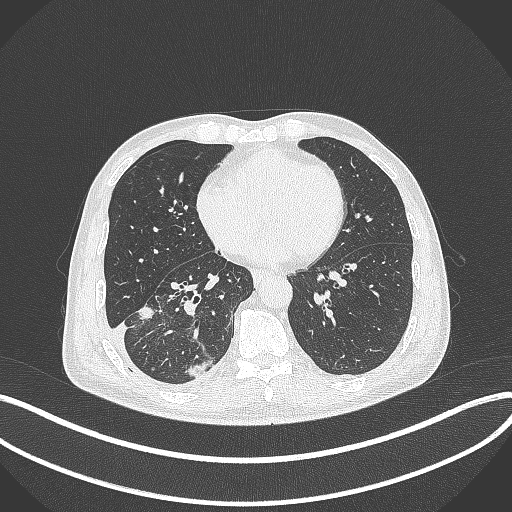
Chest CT, one axial slice. Position 148 of 388 along the scan axis. 120 kVp. Lung window (W 1500 / L -600 HU). 512 × 512 image matrix. Male patient, age 64 years. Case-level facts recorded for this patient, not image findings: clinical TNM (as recorded): T3 N0 M0.
Outlined on this slice (bounding box drawn by a radiologist):
- lung tumour (recorded histology: adenocarcinoma): bounding box (x1, y1, x2, y2) in pixels: (132, 301, 162, 324)